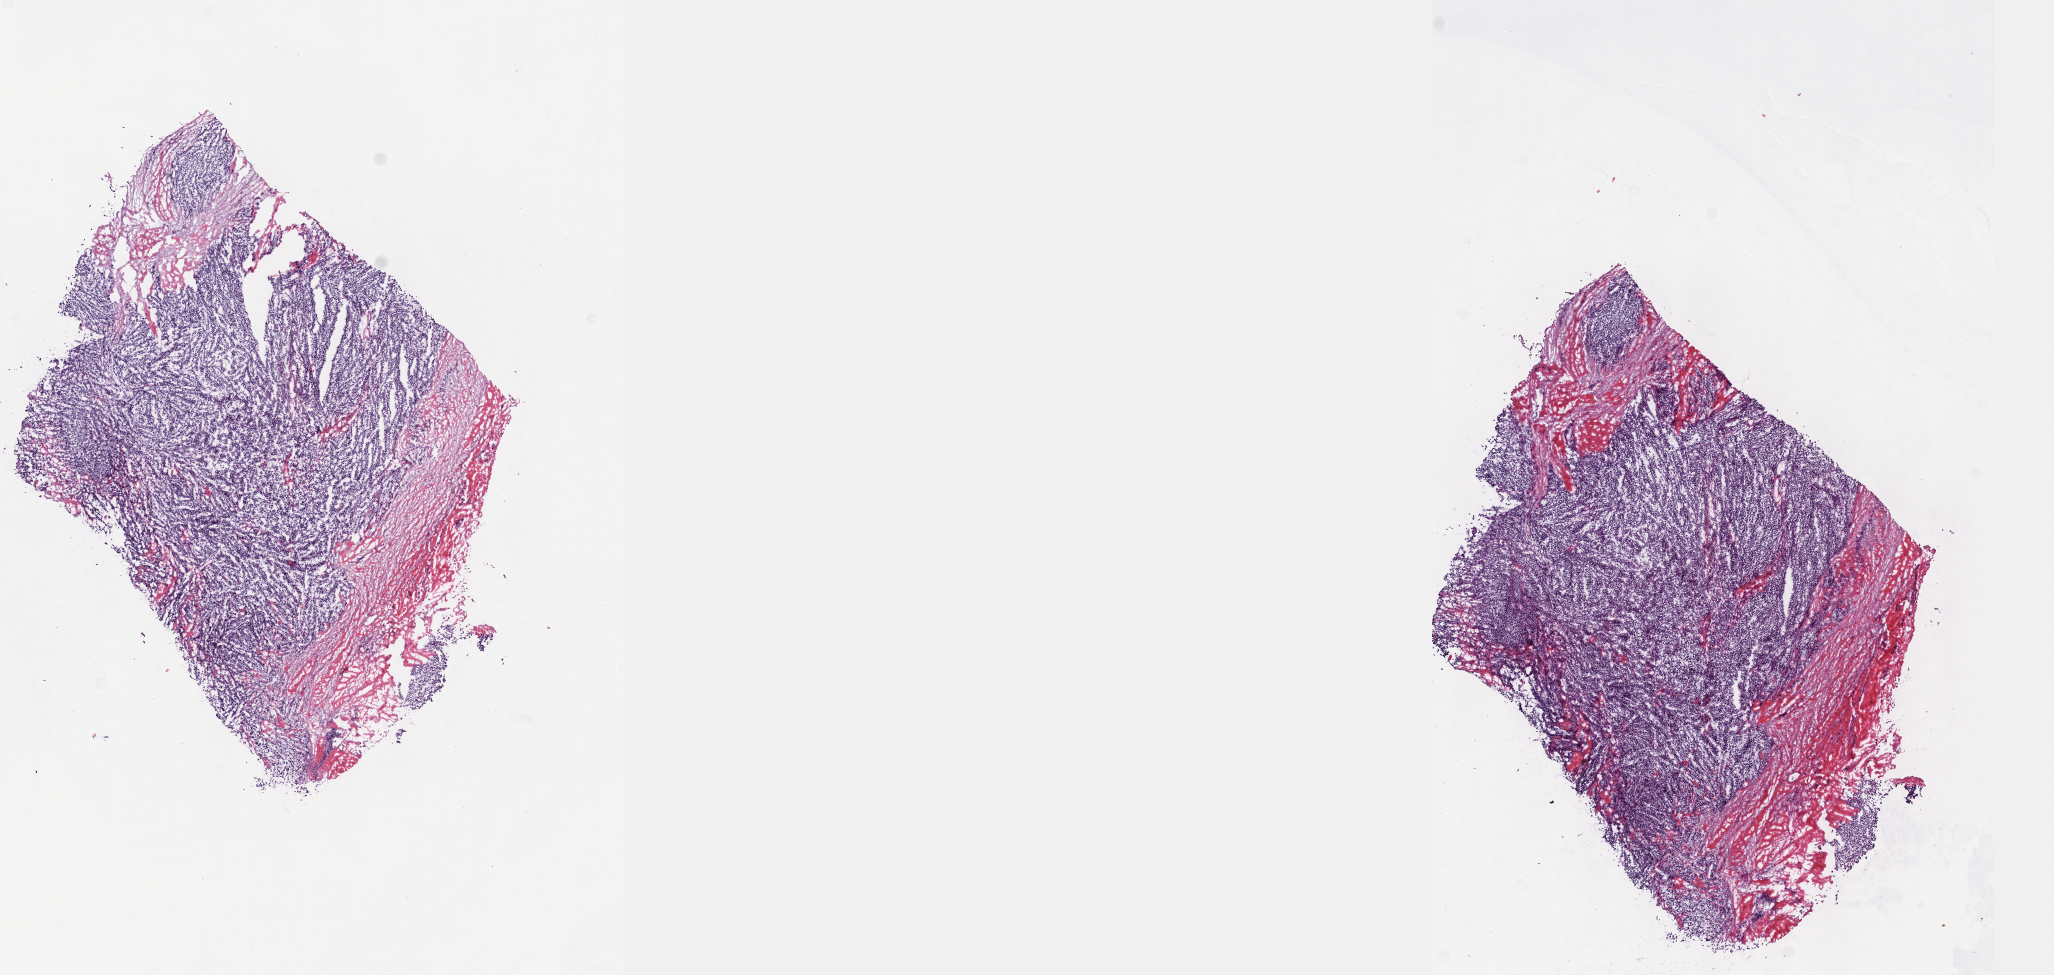
Hematoxylin and eosin (H&E) stained whole-slide image, whole scanned area (about 16.6 x 7.9 mm, acquisition: 40x scan) shown as a low-resolution overview; frozen section from the top of the tissue portion; metastatic tumour sample, sampled site not recorded. Patient: male, age at initial diagnosis 48 years. Composition of this section per pathologist review: tumour cells 90%, tumour nuclei 92%, normal cells 0%, stromal cells 10%, necrosis 0%. Inflammatory infiltration, as recorded: lymphocyte infiltration 0%, monocyte infiltration 0%, neutrophil infiltration 0%.
This section: metastatic tumour tissue. Patient diagnosis: Nodular melanoma.